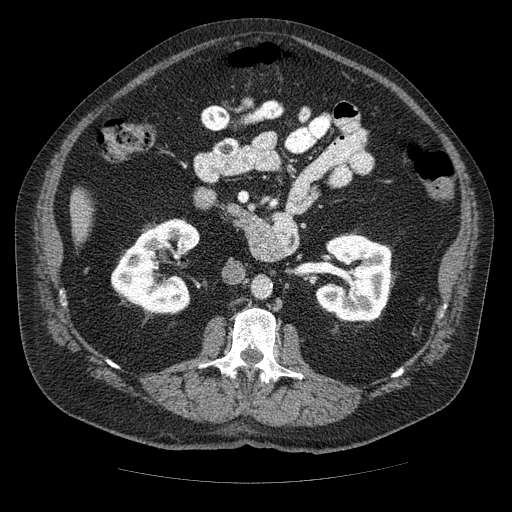
Contrast-enhanced abdominal CT (liver protocol), one axial slice. Position 7 of 85 along the scan axis. Soft-tissue window (W 400 / L 40 HU). 512 × 512 image matrix, field of view 420 × 420 mm. From the clinical record (not read from this slice): diagnosis: hepatocellular carcinoma (patient treated with transarterial chemoembolisation; whether this scan precedes or follows treatment is not stated here); TNM stage (as recorded): Stage-IIIA; Child-Pugh class: A; tumour nodularity: multinodular; tumour size: 7 cm.
Structures marked on this image (semi-automatic segmentation, software-assisted and operator-edited):
- liver parenchyma outside the tumour (the mass and vessels are separate outlines, so this box may not span the whole liver): bounding box [x1, y1, x2, y2] px = [70, 190, 92, 240]